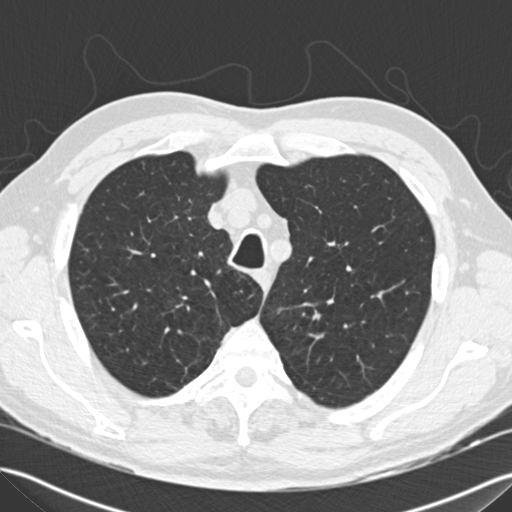
Chest CT (low-dose screening protocol), one axial image, baseline annual screen, lung window (W 1500 / L -600 HU), standard (soft-tissue) reconstruction kernel (B30f), 120 kVp, slice 41 of 197 in the series. Male, age 66 years at enrolment.
Expert-annotated lung lesion, bounding box (x1, y1, x2, y2) in pixels: (292, 299, 336, 340). Screening reader's record for this exam: no non-calcified nodule ≥4 mm recorded. Later outcome: lung cancer diagnosed 679 days after this screen — squamous cell carcinoma, NOS, left upper lobe, poorly differentiated (G3), stage IA (AJCC 6th edition), 15 mm at pathology.